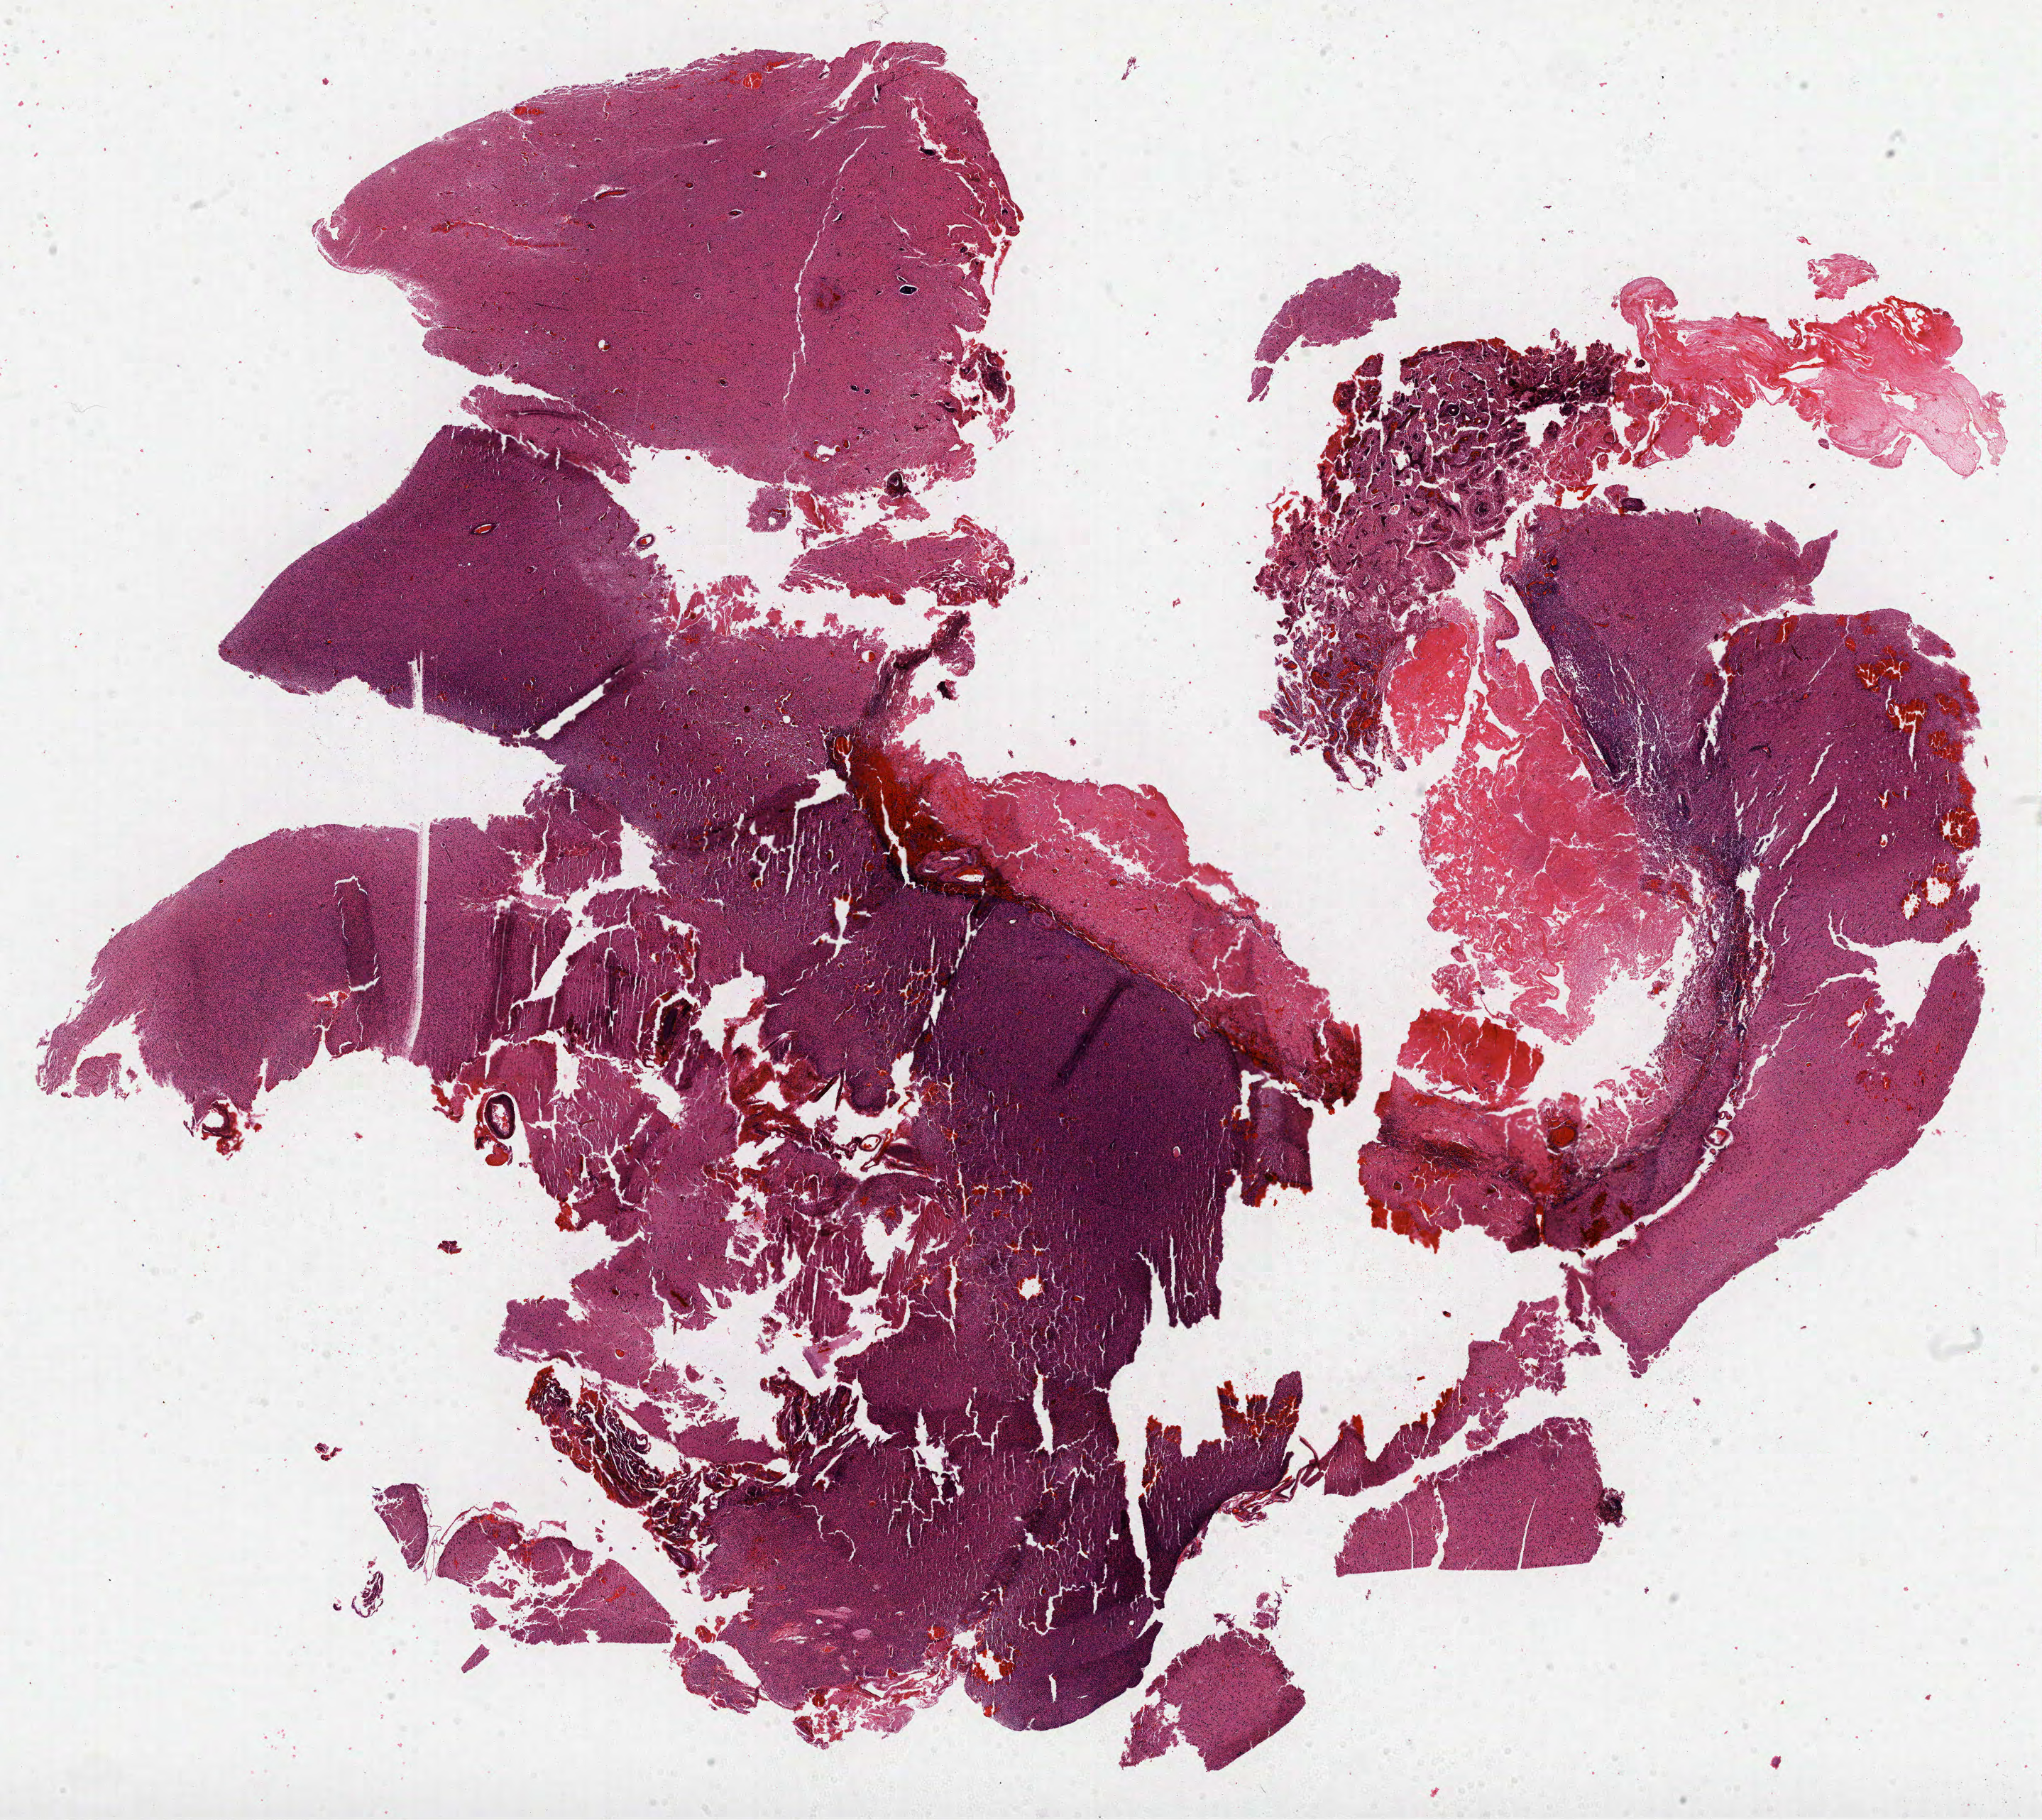
Digitized H&E-stained tissue section (whole slide), whole scanned area (about 23.2 x 20.7 mm, slide scanned at 40x) shown as a low-resolution overview, formalin-fixed paraffin-embedded (FFPE) diagnostic section, primary tumour sample from the brain. Female, age 52 years at initial diagnosis.
Pathologic diagnosis: Glioblastoma.